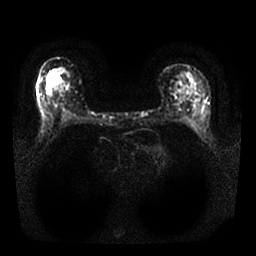
Breast MRI, one axial slice. Slice 15 of 25 in the series (ordered by position). Diffusion-weighted series; image 2 of 4 stored at this slice position (different b-values; order by instance number). 1.5 T. 4 mm slice thickness. 256 × 256 image matrix. Female patient.
Annotated regions visible in this slice (manually delineated by an expert):
- tumour on diffusion-weighted imaging: bounding box [x1, y1, x2, y2] px = [56, 77, 60, 81]